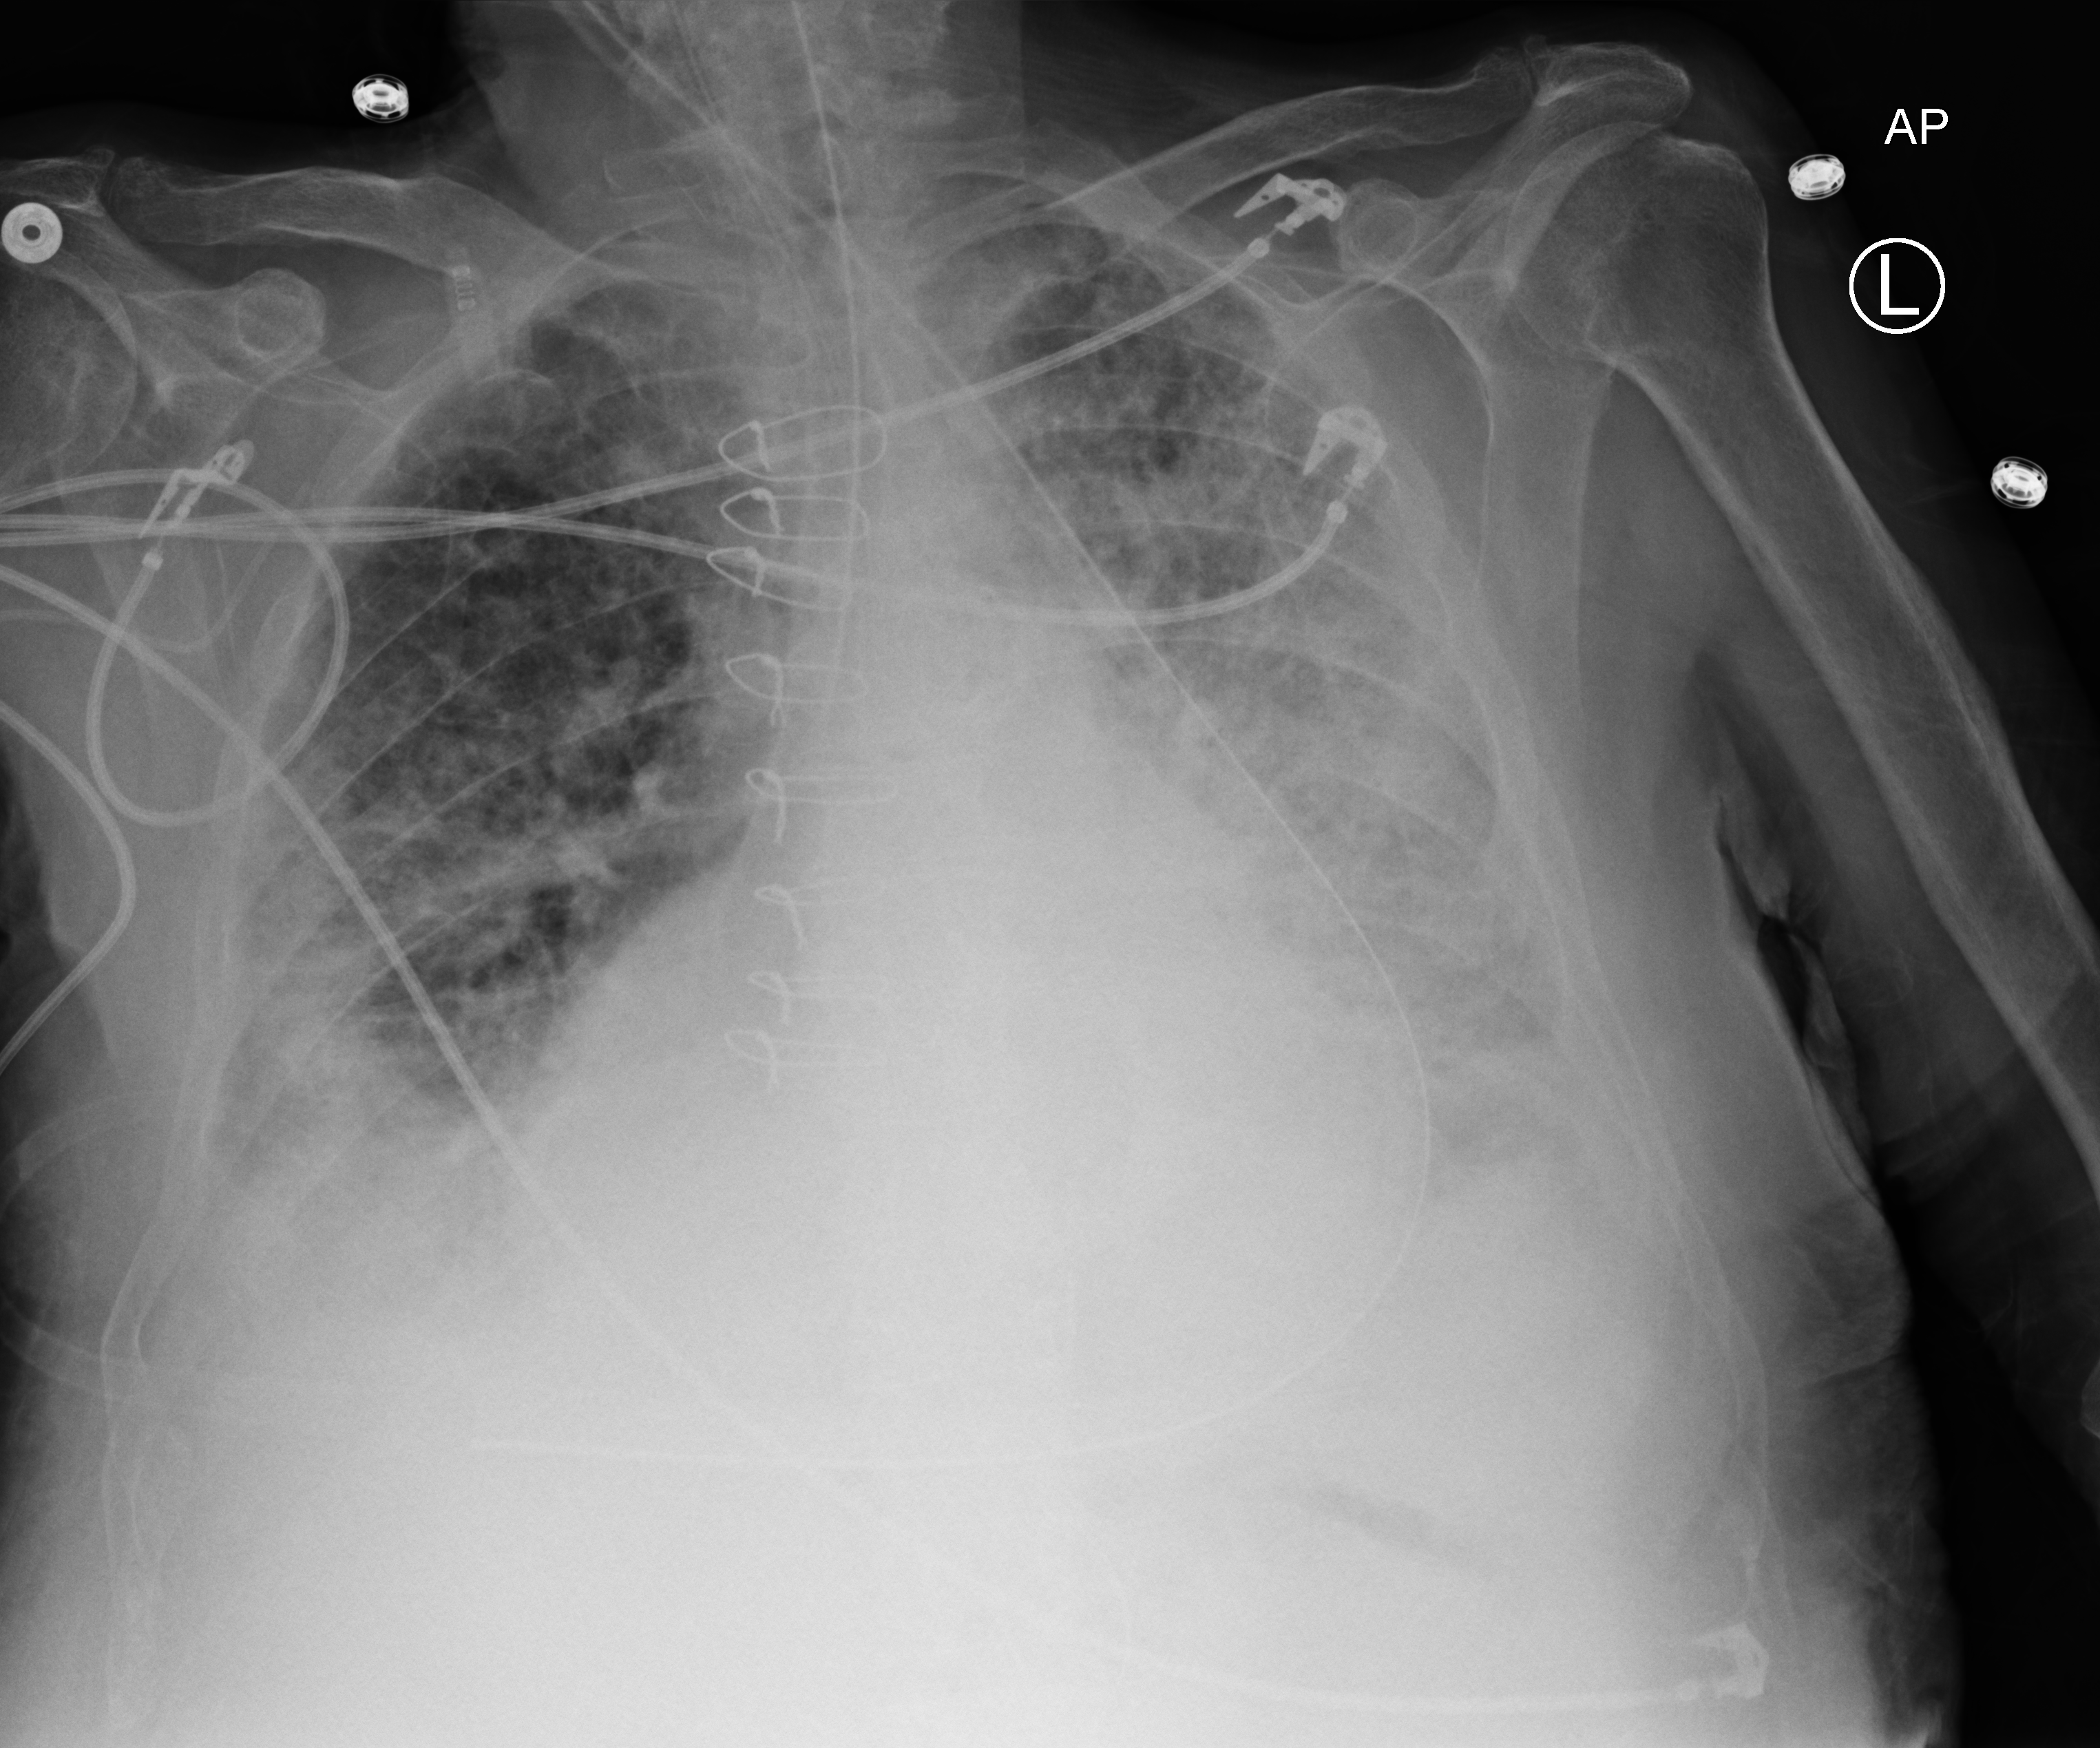
Portable chest radiograph. Patient hospitalised with COVID-19; male, aged 75–90 years.
Admission-level facts for this patient (not findings on this image; timing relative to this image not recorded):
- admitted to intensive care during this hospital stay: yes